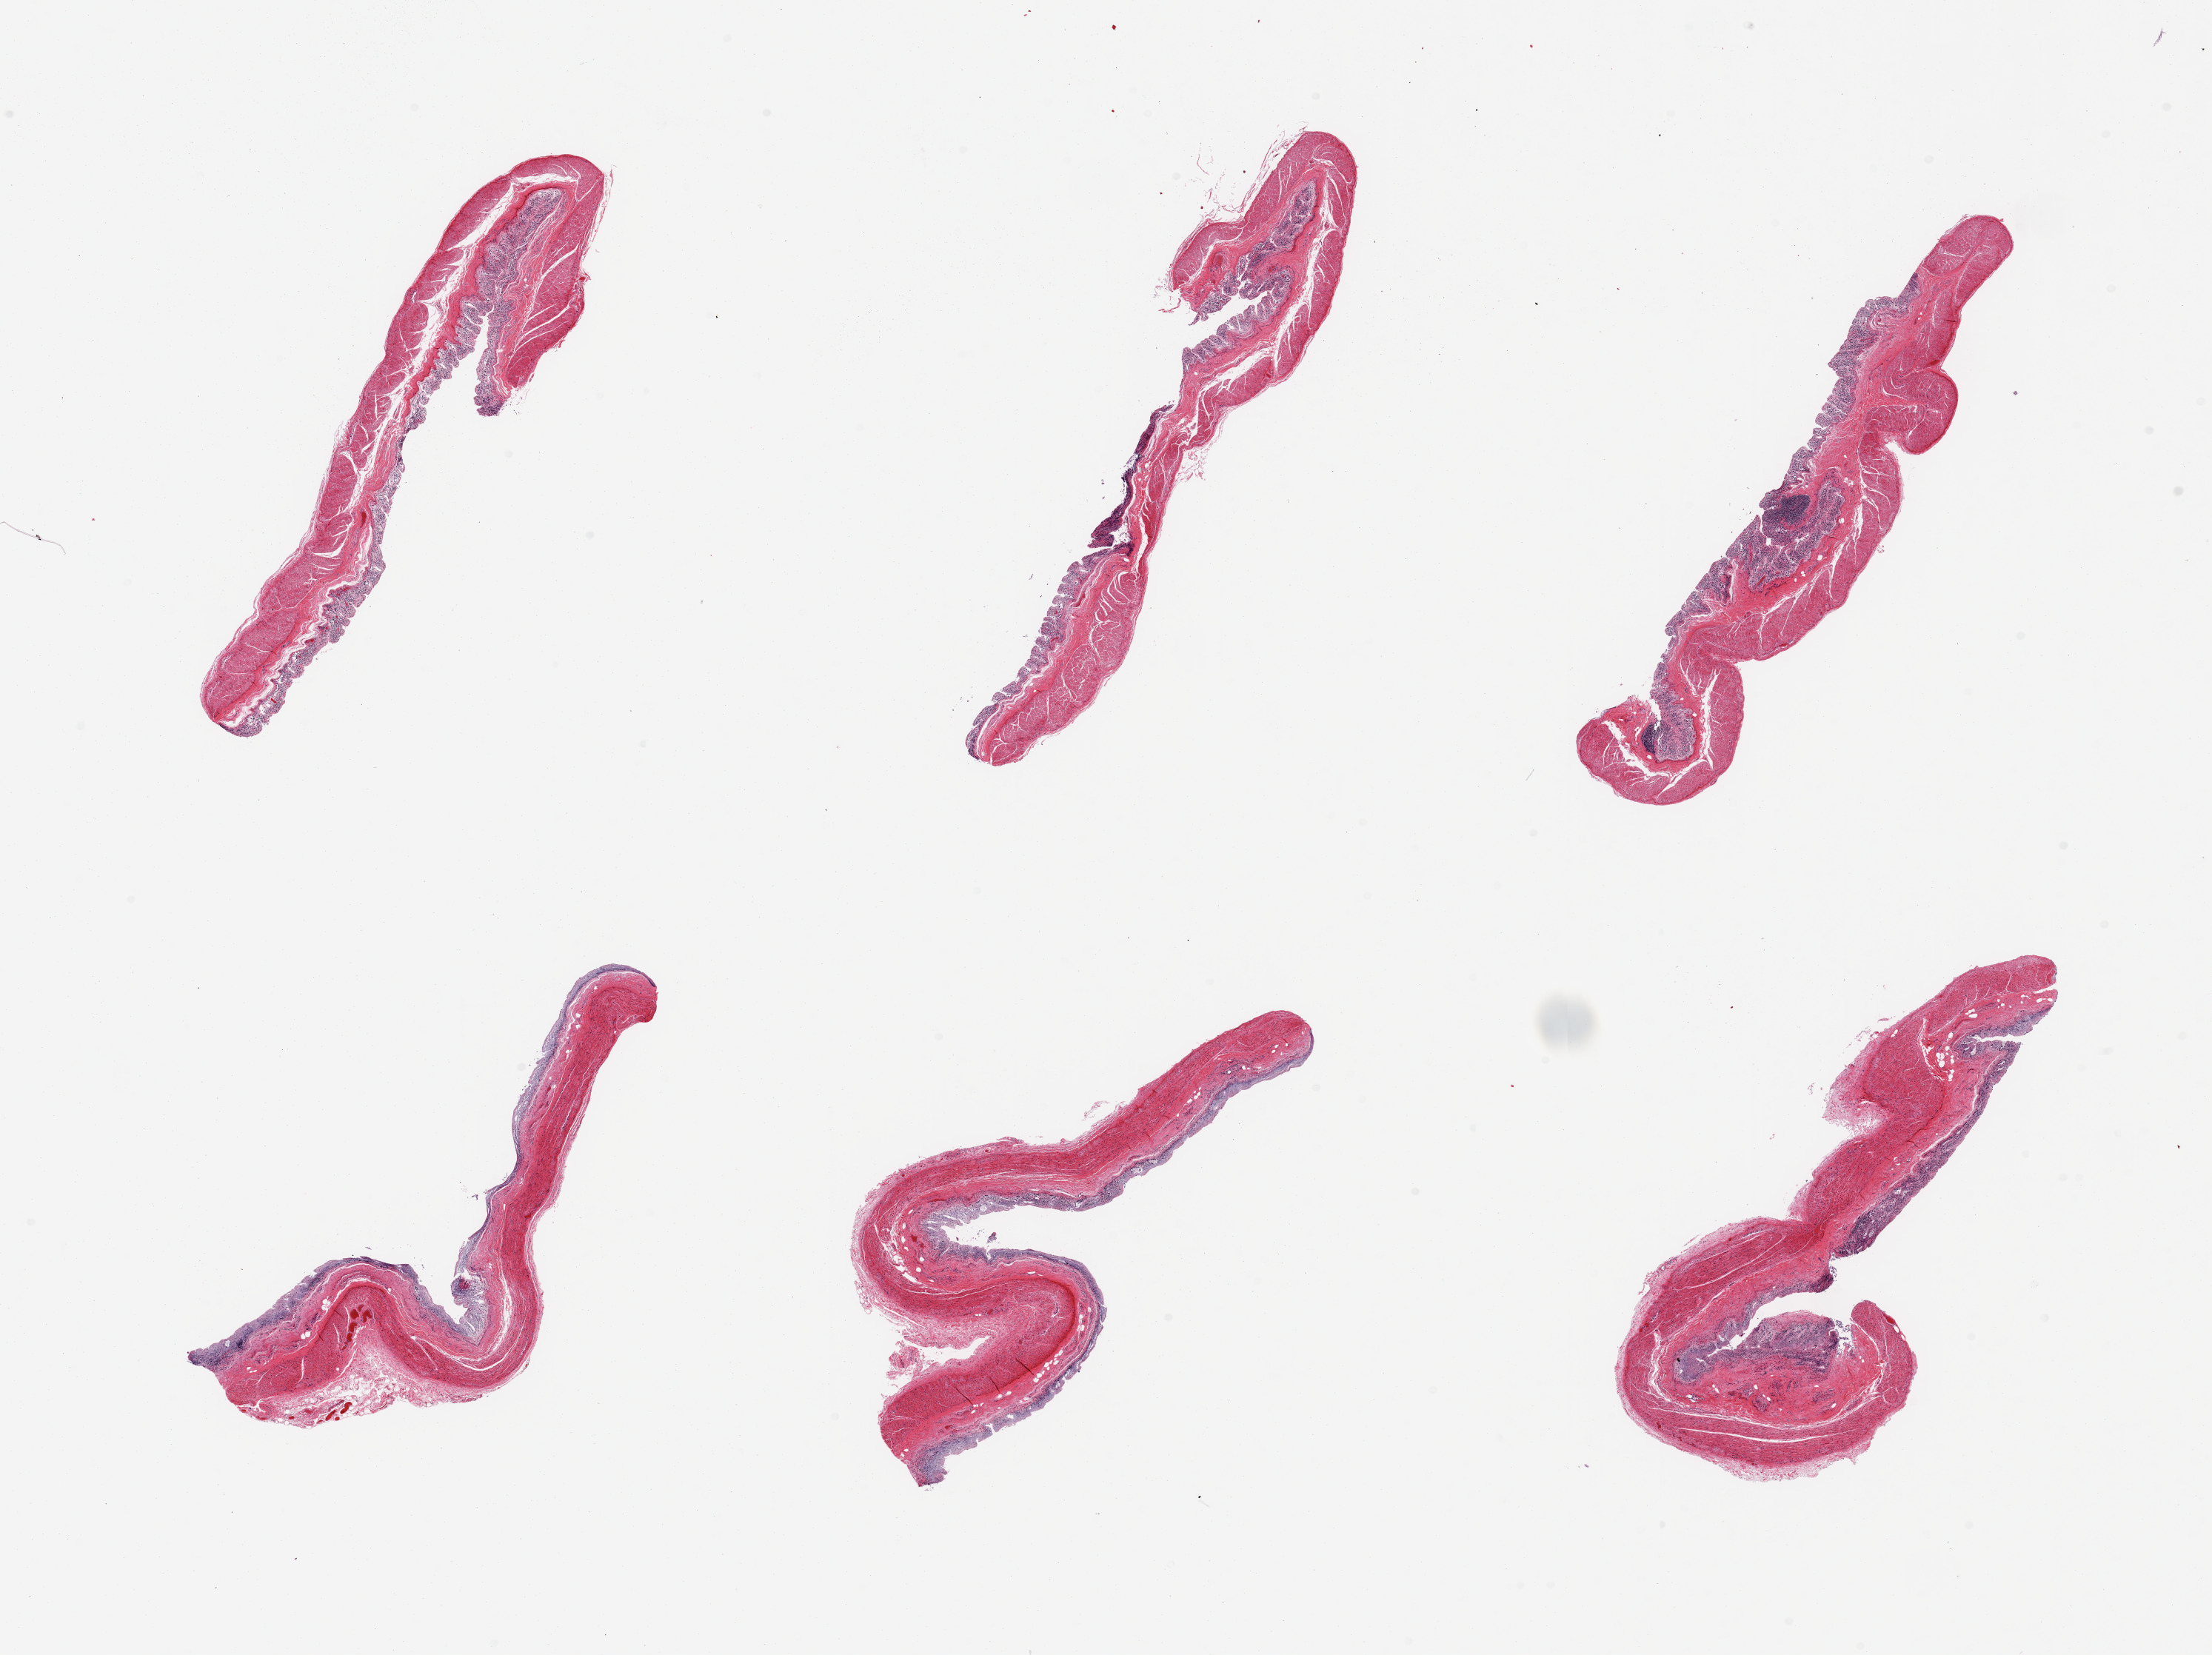
Digitized H&E-stained section, a low-resolution overview of the entire scanned area, about 23.6 x 17.7 mm, PAXgene-fixed, paraffin-embedded tissue, section of transverse colon (target tissue), tissue donor sample. Donor: male.
Pathologist's review note for this sample: 6 pieces; severely autolyzed mucosa, moderately autolyzed muscularis.